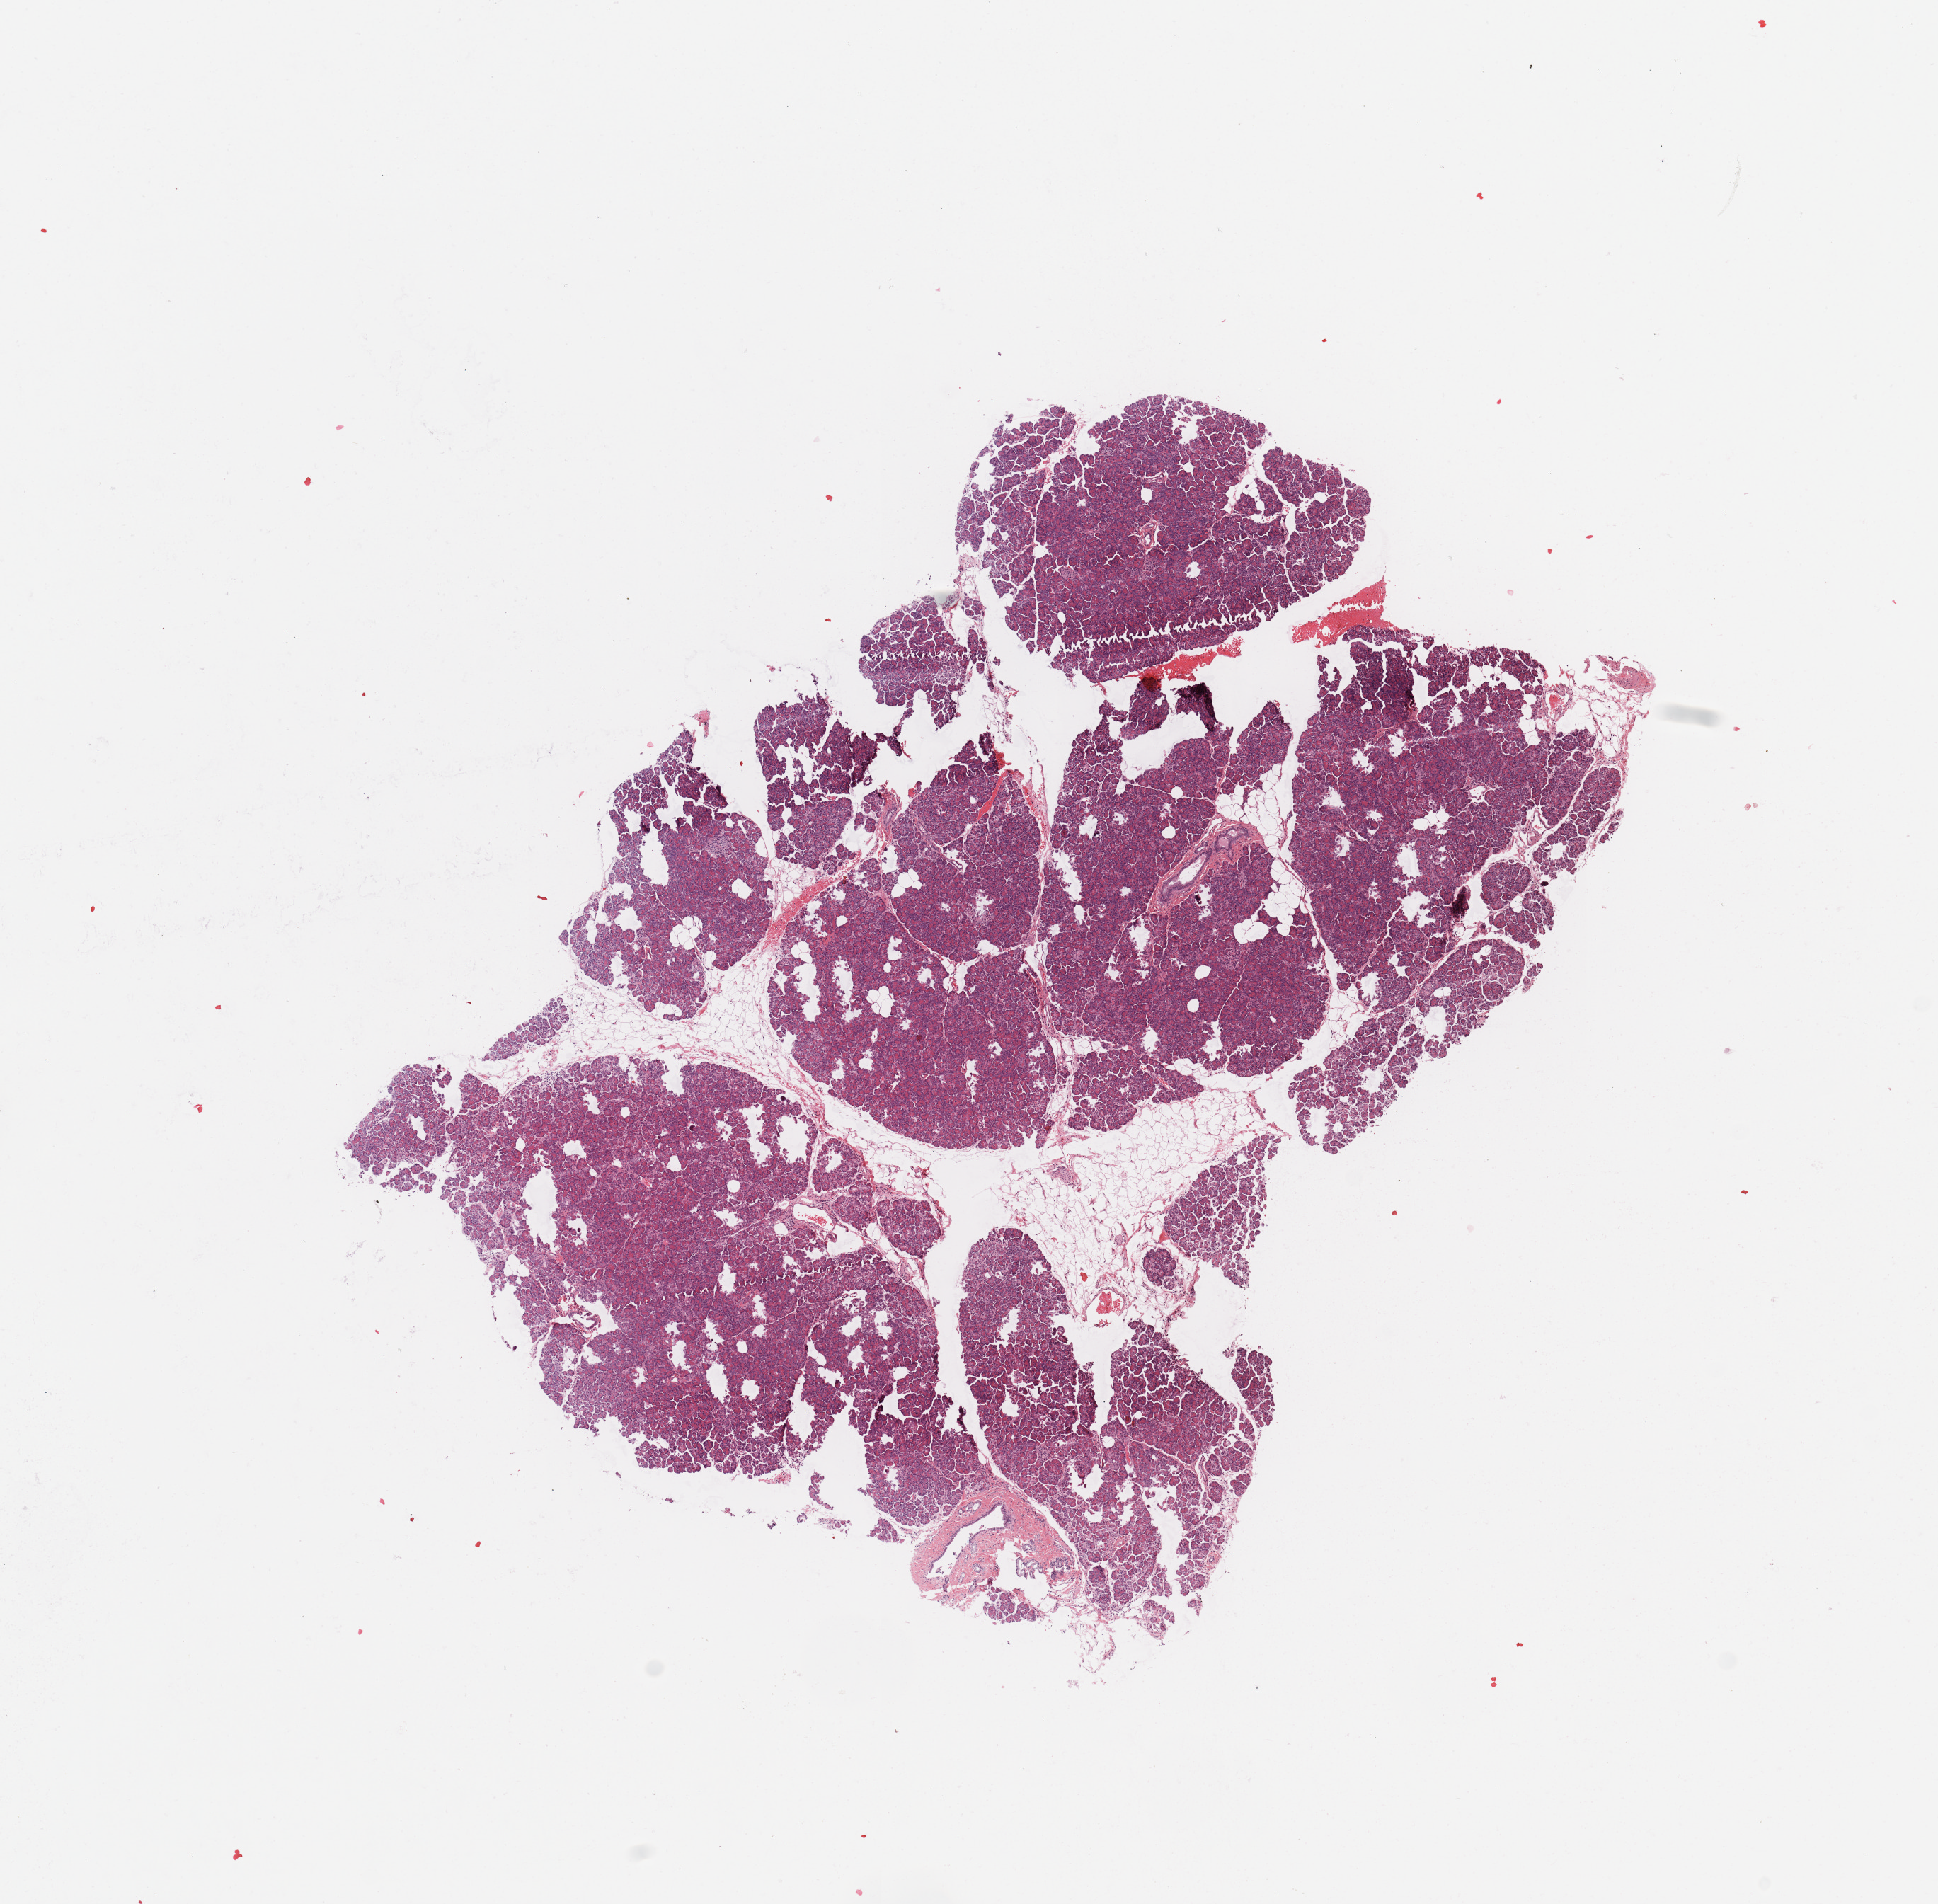
Hematoxylin and eosin (H&E) stained whole-slide image, low-resolution overview of the scanned area, about 10.8 x 10.6 mm (slide scanned at 20x). Normal (non-tumour) tissue sample, sampled site: pancreas. Female, 64 y/o.
This section: normal (non-tumour) tissue from the same patient. Patient diagnosis: Infiltrating duct carcinoma, NOS.